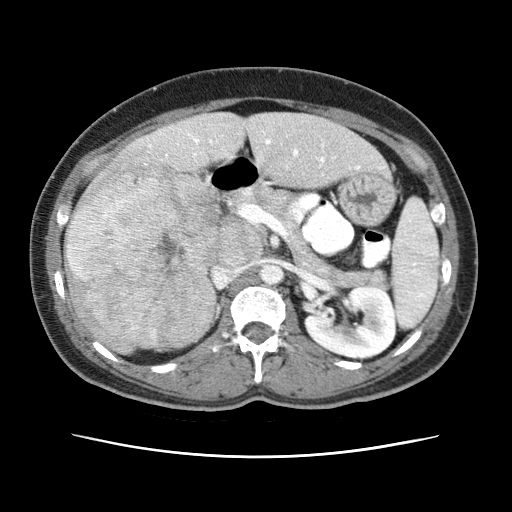
Contrast-enhanced abdominal CT (liver protocol), one axial slice; slice 24 of 79 in the series (ordered by position); reconstruction kernel STANDARD; soft-tissue window (W 400 / L 40 HU); 2.5 mm slice thickness; 512 × 512 image matrix, field of view 340 × 340 mm. From the clinical record (not read from this slice): diagnosis: hepatocellular carcinoma (patient treated with transarterial chemoembolisation; whether this scan precedes or follows treatment is not stated here); TNM stage (as recorded): Stage-I; Child-Pugh class: A; tumour differentiation: moderately differentiated; tumour nodularity: uninodular.
Outlined on this slice (semi-automatic segmentation, software-assisted and operator-edited):
- abdominal aorta: box from (x=262, y=266) to (x=282, y=284) px
- liver parenchyma outside the tumour (the mass and vessels are separate outlines, so this box may not span the whole liver): (x=64, y=112)–(x=384, y=311)
- mass: (x=64, y=162)–(x=217, y=355)
- liver vessels: (x=149, y=134)–(x=359, y=169)